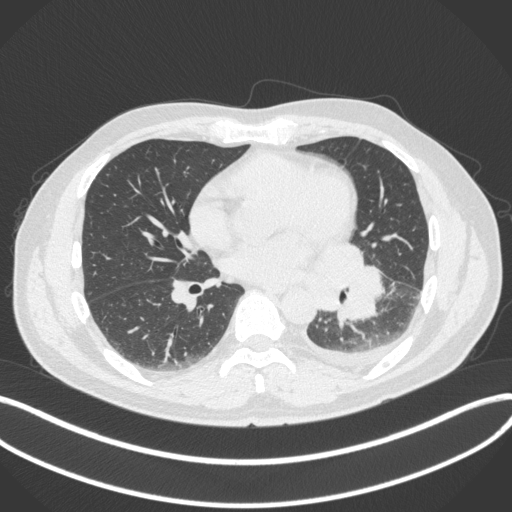
Chest CT, one axial slice. Slice 164 of 350 in the series (ordered by position). Reconstruction kernel B31f. 120 kVp. Lung window (W 1500 / L -600 HU). 1 mm slice thickness. 512 × 512 image matrix. Patient: male, 58 years. Case-level facts recorded for this patient, not image findings: clinical TNM (as recorded): T3 N1 M1b; histopathological grade: G3.
Structures marked on this image (rectangle marked by the reading radiologist):
- lung tumour (recorded histology: small cell carcinoma): bounding box (x1, y1, x2, y2) in pixels: (315, 238, 387, 328)